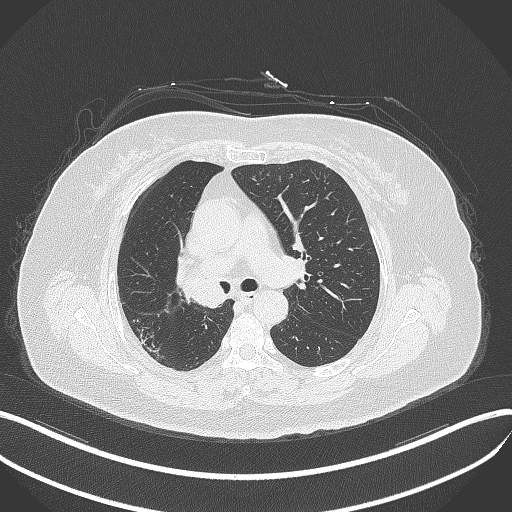
Chest CT, one axial slice. Slice 227 of 376 in the series (ordered by position). 120 kVp. Lung window (W 1500 / L -600 HU). 1 mm slice thickness. 512 × 512 image matrix. Female patient, age 60 years. Case-level facts recorded for this patient, not image findings: clinical TNM (as recorded): T1c N0 M0.
Structures marked on this image (bounding box drawn by a radiologist):
- lung tumour (recorded histology: squamous cell carcinoma): bounding box [x1, y1, x2, y2] px = [171, 263, 231, 311]